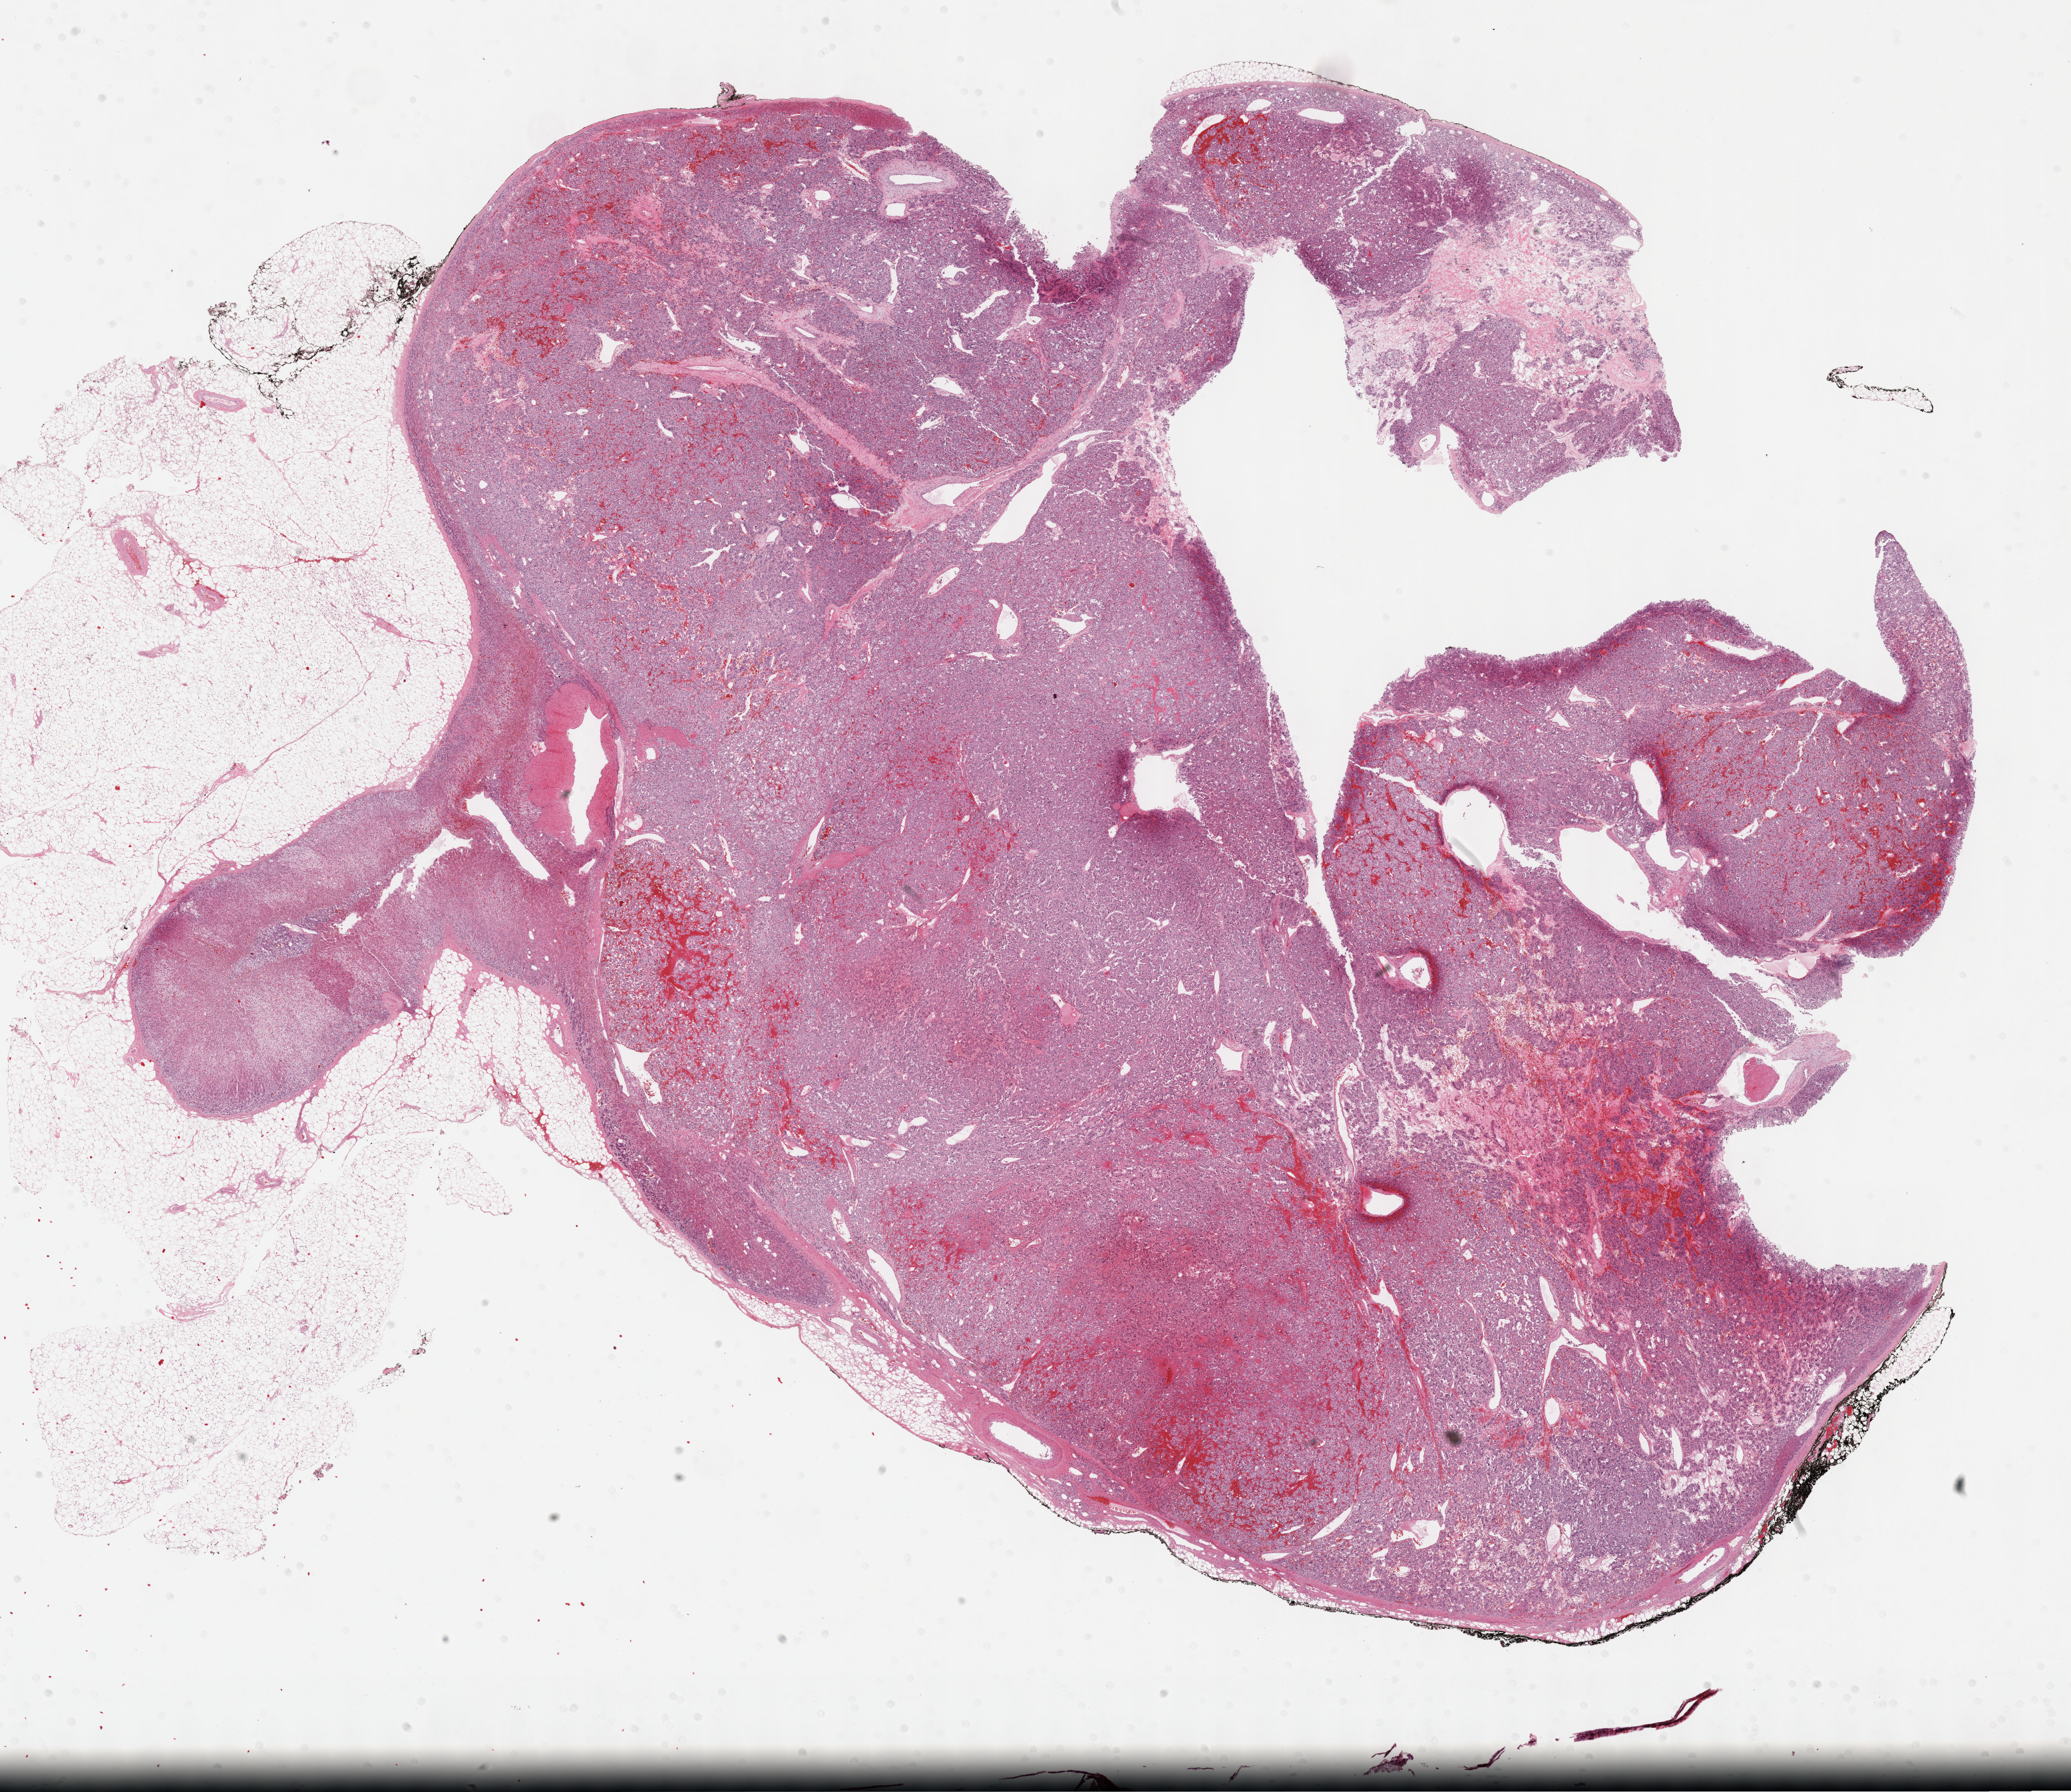
Digitized Hematoxylin and eosin (H&E) stained tissue section (whole slide), low-resolution overview of the scanned area, about 25.2 x 21.8 mm, formalin-fixed paraffin-embedded (FFPE) diagnostic section, sample: primary tumour, adrenal gland. Male patient; age at initial diagnosis 59 years.
Pathologic diagnosis: Pheochromocytoma, NOS.